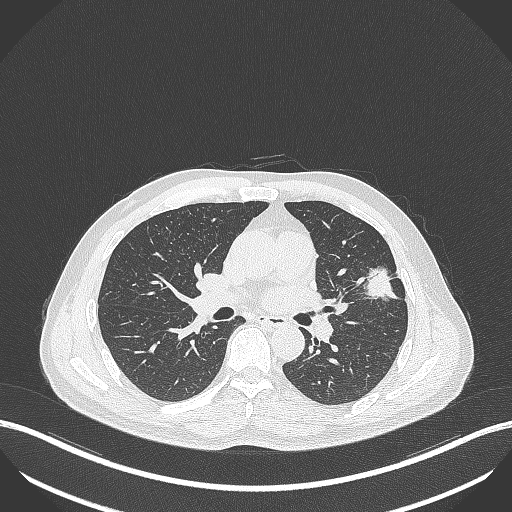
Chest CT, one axial slice; position 219 of 418 along the scan axis; 120 kVp; lung window (W 1500 / L -600 HU); 512 × 512 image matrix, field of view 400 × 400 mm. Patient: male, 55 years. From the clinical record (not read from this slice): clinical TNM (as recorded): T1c N0 M0; histopathological grade: G2-3.
Structures marked on this image (rectangle marked by the reading radiologist):
- lung tumour (recorded histology: adenocarcinoma): bounding box [x1, y1, x2, y2] px = [362, 266, 402, 305]